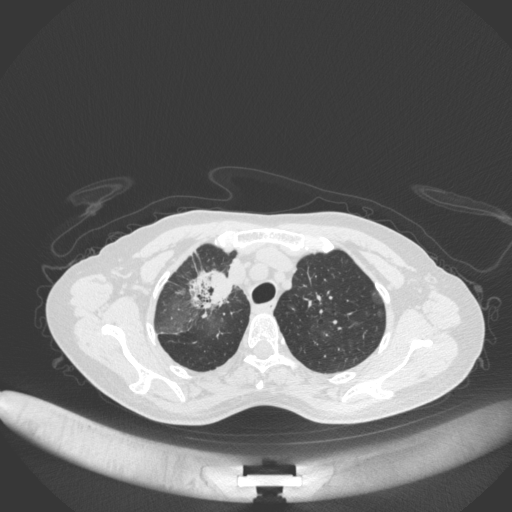
Chest CT, one axial slice. Slice 258 of 311 in the series (ordered by position). Reconstruction kernel B31f. Lung window (W 1500 / L -600 HU). 512 × 512 image matrix, field of view 400 × 400 mm. Patient: female, 59 years. Case-level facts recorded for this patient, not image findings: clinical TNM (as recorded): T3 N0 M0.
Structures marked on this image (rectangle marked by the reading radiologist):
- lung tumour (recorded histology: adenocarcinoma): box from (x=186, y=268) to (x=238, y=319) px